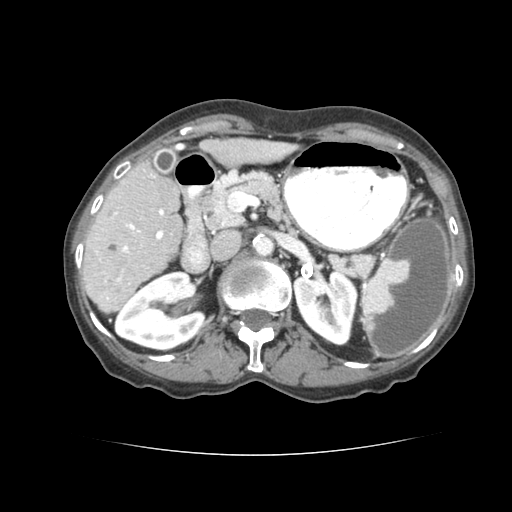
Contrast-enhanced abdominal CT (liver protocol), one axial slice; position 34 of 77 along the scan axis; 120 kVp; soft-tissue window (W 400 / L 40 HU); 2.5 mm slice thickness; 512 × 512 image matrix, field of view 340 × 340 mm. Case-level facts recorded for this patient, not image findings: diagnosis: hepatocellular carcinoma (patient treated with transarterial chemoembolisation; whether this scan precedes or follows treatment is not stated here); TNM stage (as recorded): Stage-I; Child-Pugh class: A; tumour size: 7.6 cm.
Annotated regions visible in this slice (semi-automatically segmented with operator editing):
- liver parenchyma outside the tumour (the mass and vessels are separate outlines, so this box may not span the whole liver): bounding box [x1, y1, x2, y2] px = [80, 142, 294, 314]
- liver vessels: [101, 206, 164, 278]